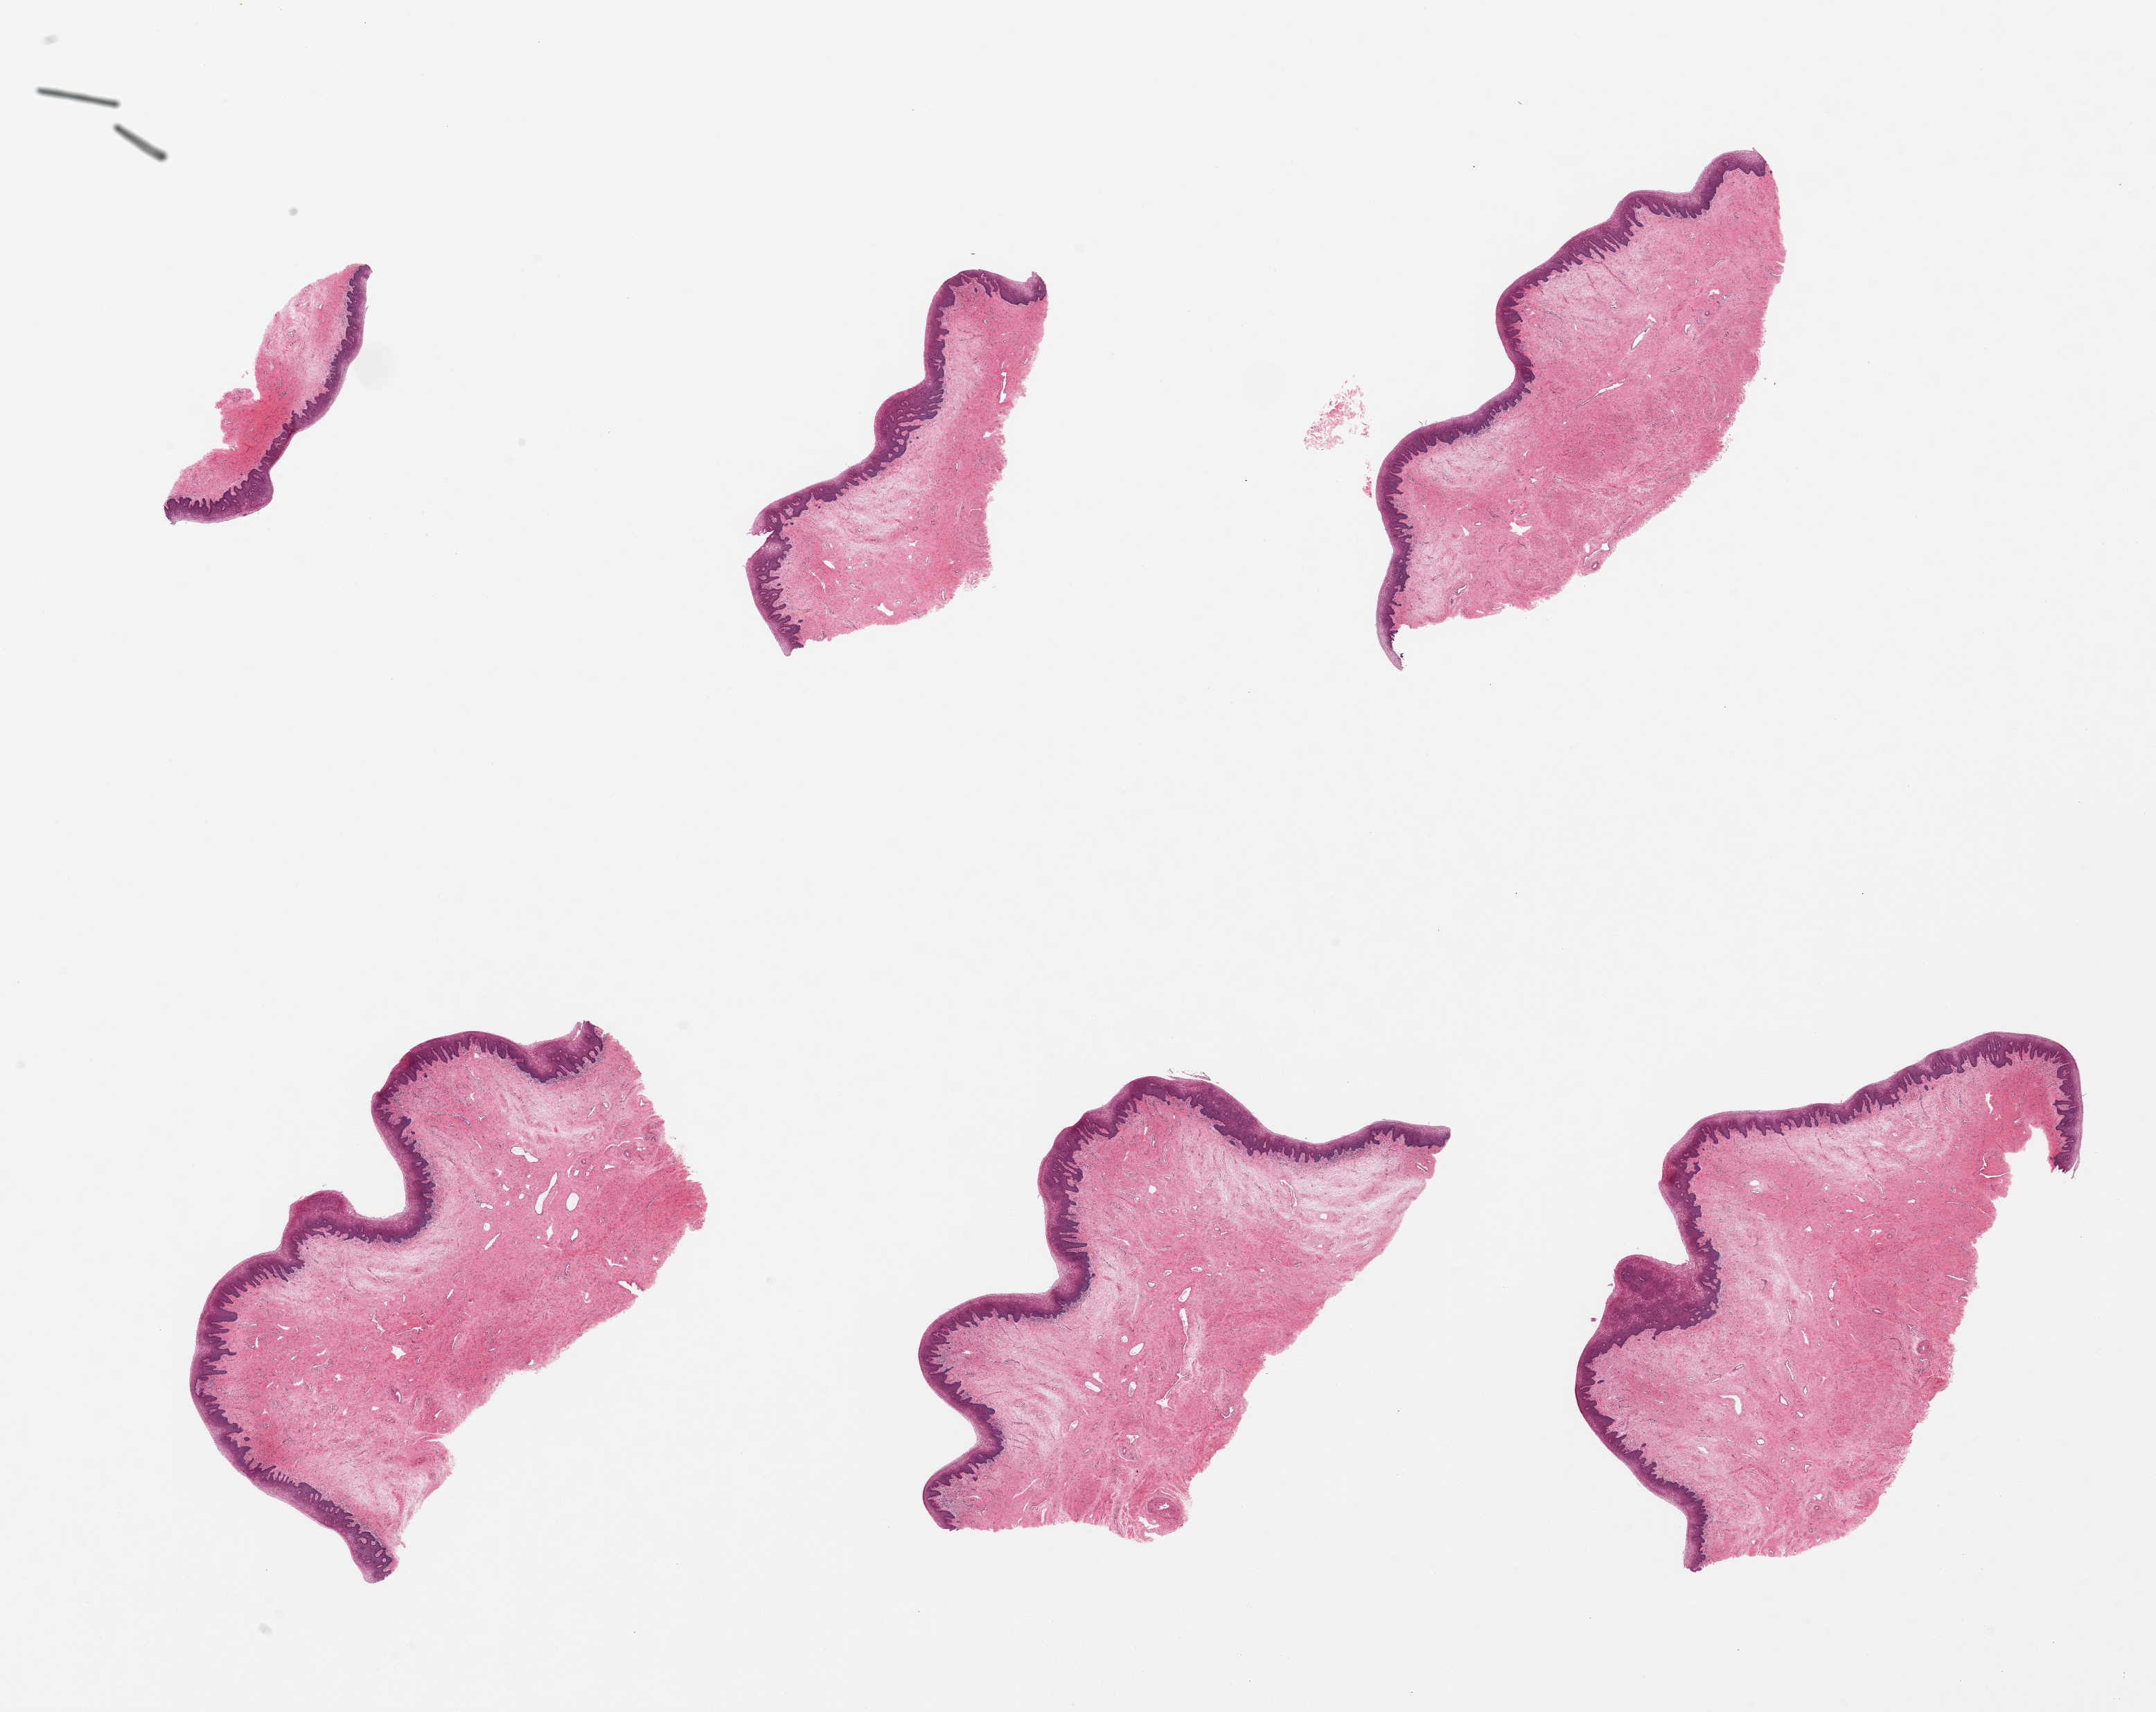
Hematoxylin and eosin (H&E) whole-slide image, brightfield, shown as a low-resolution overview of the whole scanned area (about 24.6 x 19.5 mm, from a 20x scan); PAXgene-fixed paraffin-embedded (PFPE) section; target tissue: vagina; donor tissue sample. Female donor.
• pathologist's review note for this sample: 6 pieces